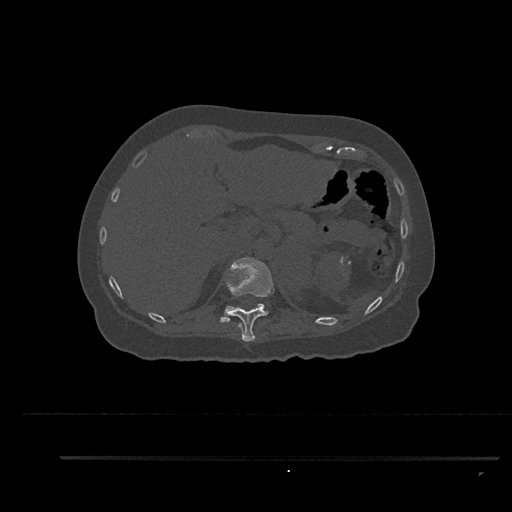
CT including the spine, one axial slice. Position 301 of 797 along the scan axis. Reconstruction kernel Br40s/3. Bone window (W 1800 / L 400 HU). 0.5 mm slice thickness. 512 × 512 image matrix, field of view 408 × 408 mm. Patient: female, 44 years. From the clinical record (not read from this slice): primary cancer: renal; vertebrae with lytic lesions (as recorded): L1.
Structures marked on this image (semi-automatically segmented with operator editing):
- T11 vertebra: bounding box (x1, y1, x2, y2) in pixels: (226, 257, 275, 343)
- T12 vertebra: (219, 304, 265, 323)